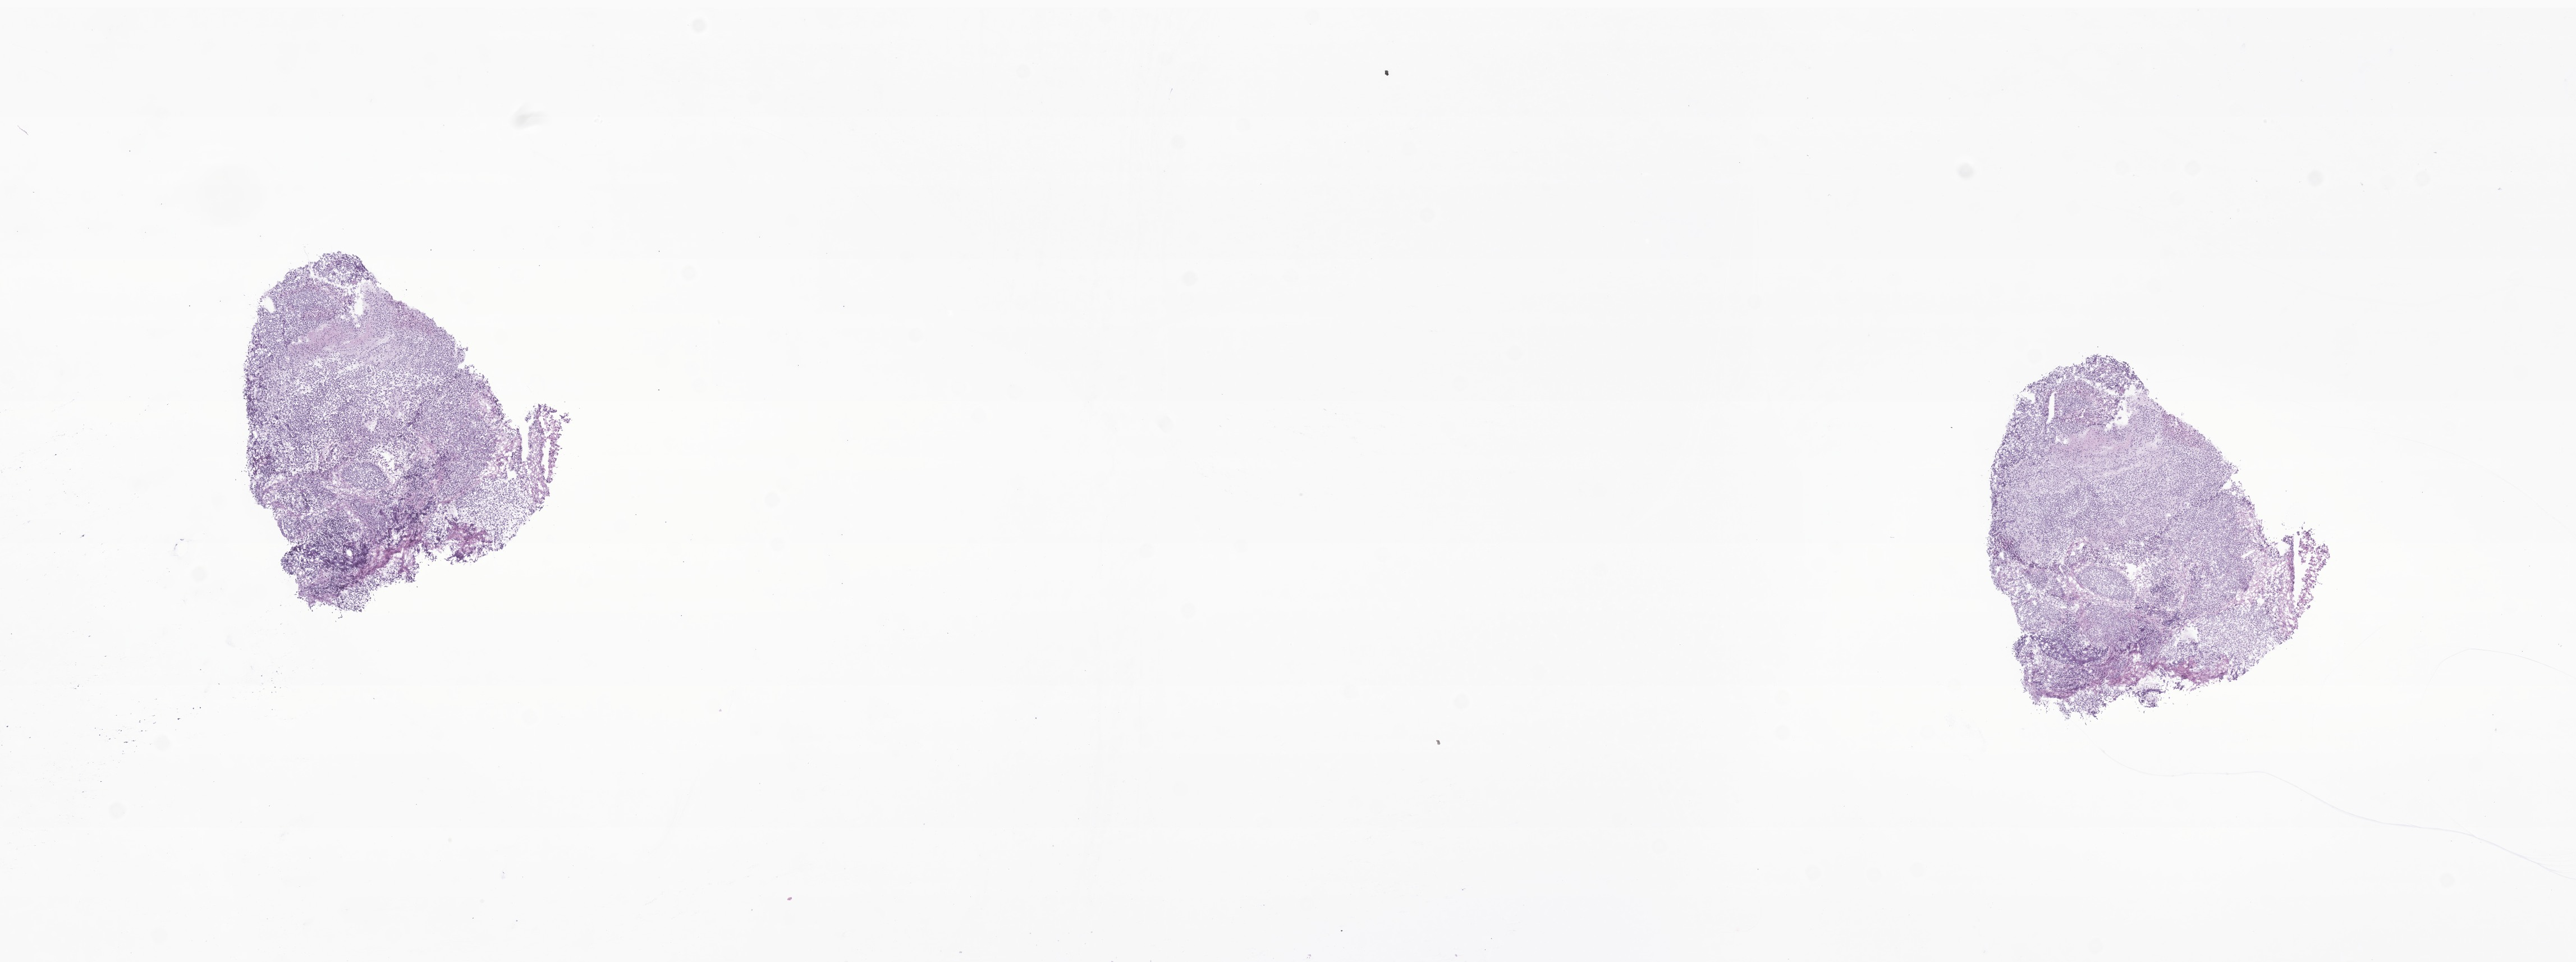
Digitized H&E-stained section of tumor tissue from the brain — shown as a low-resolution overview of the whole scanned area (about 19.3 x 7.2 mm), frozen section. Patient male; age 111 months (9 years 3 months).
Recorded diagnosis: Medulloblastoma, NOS.